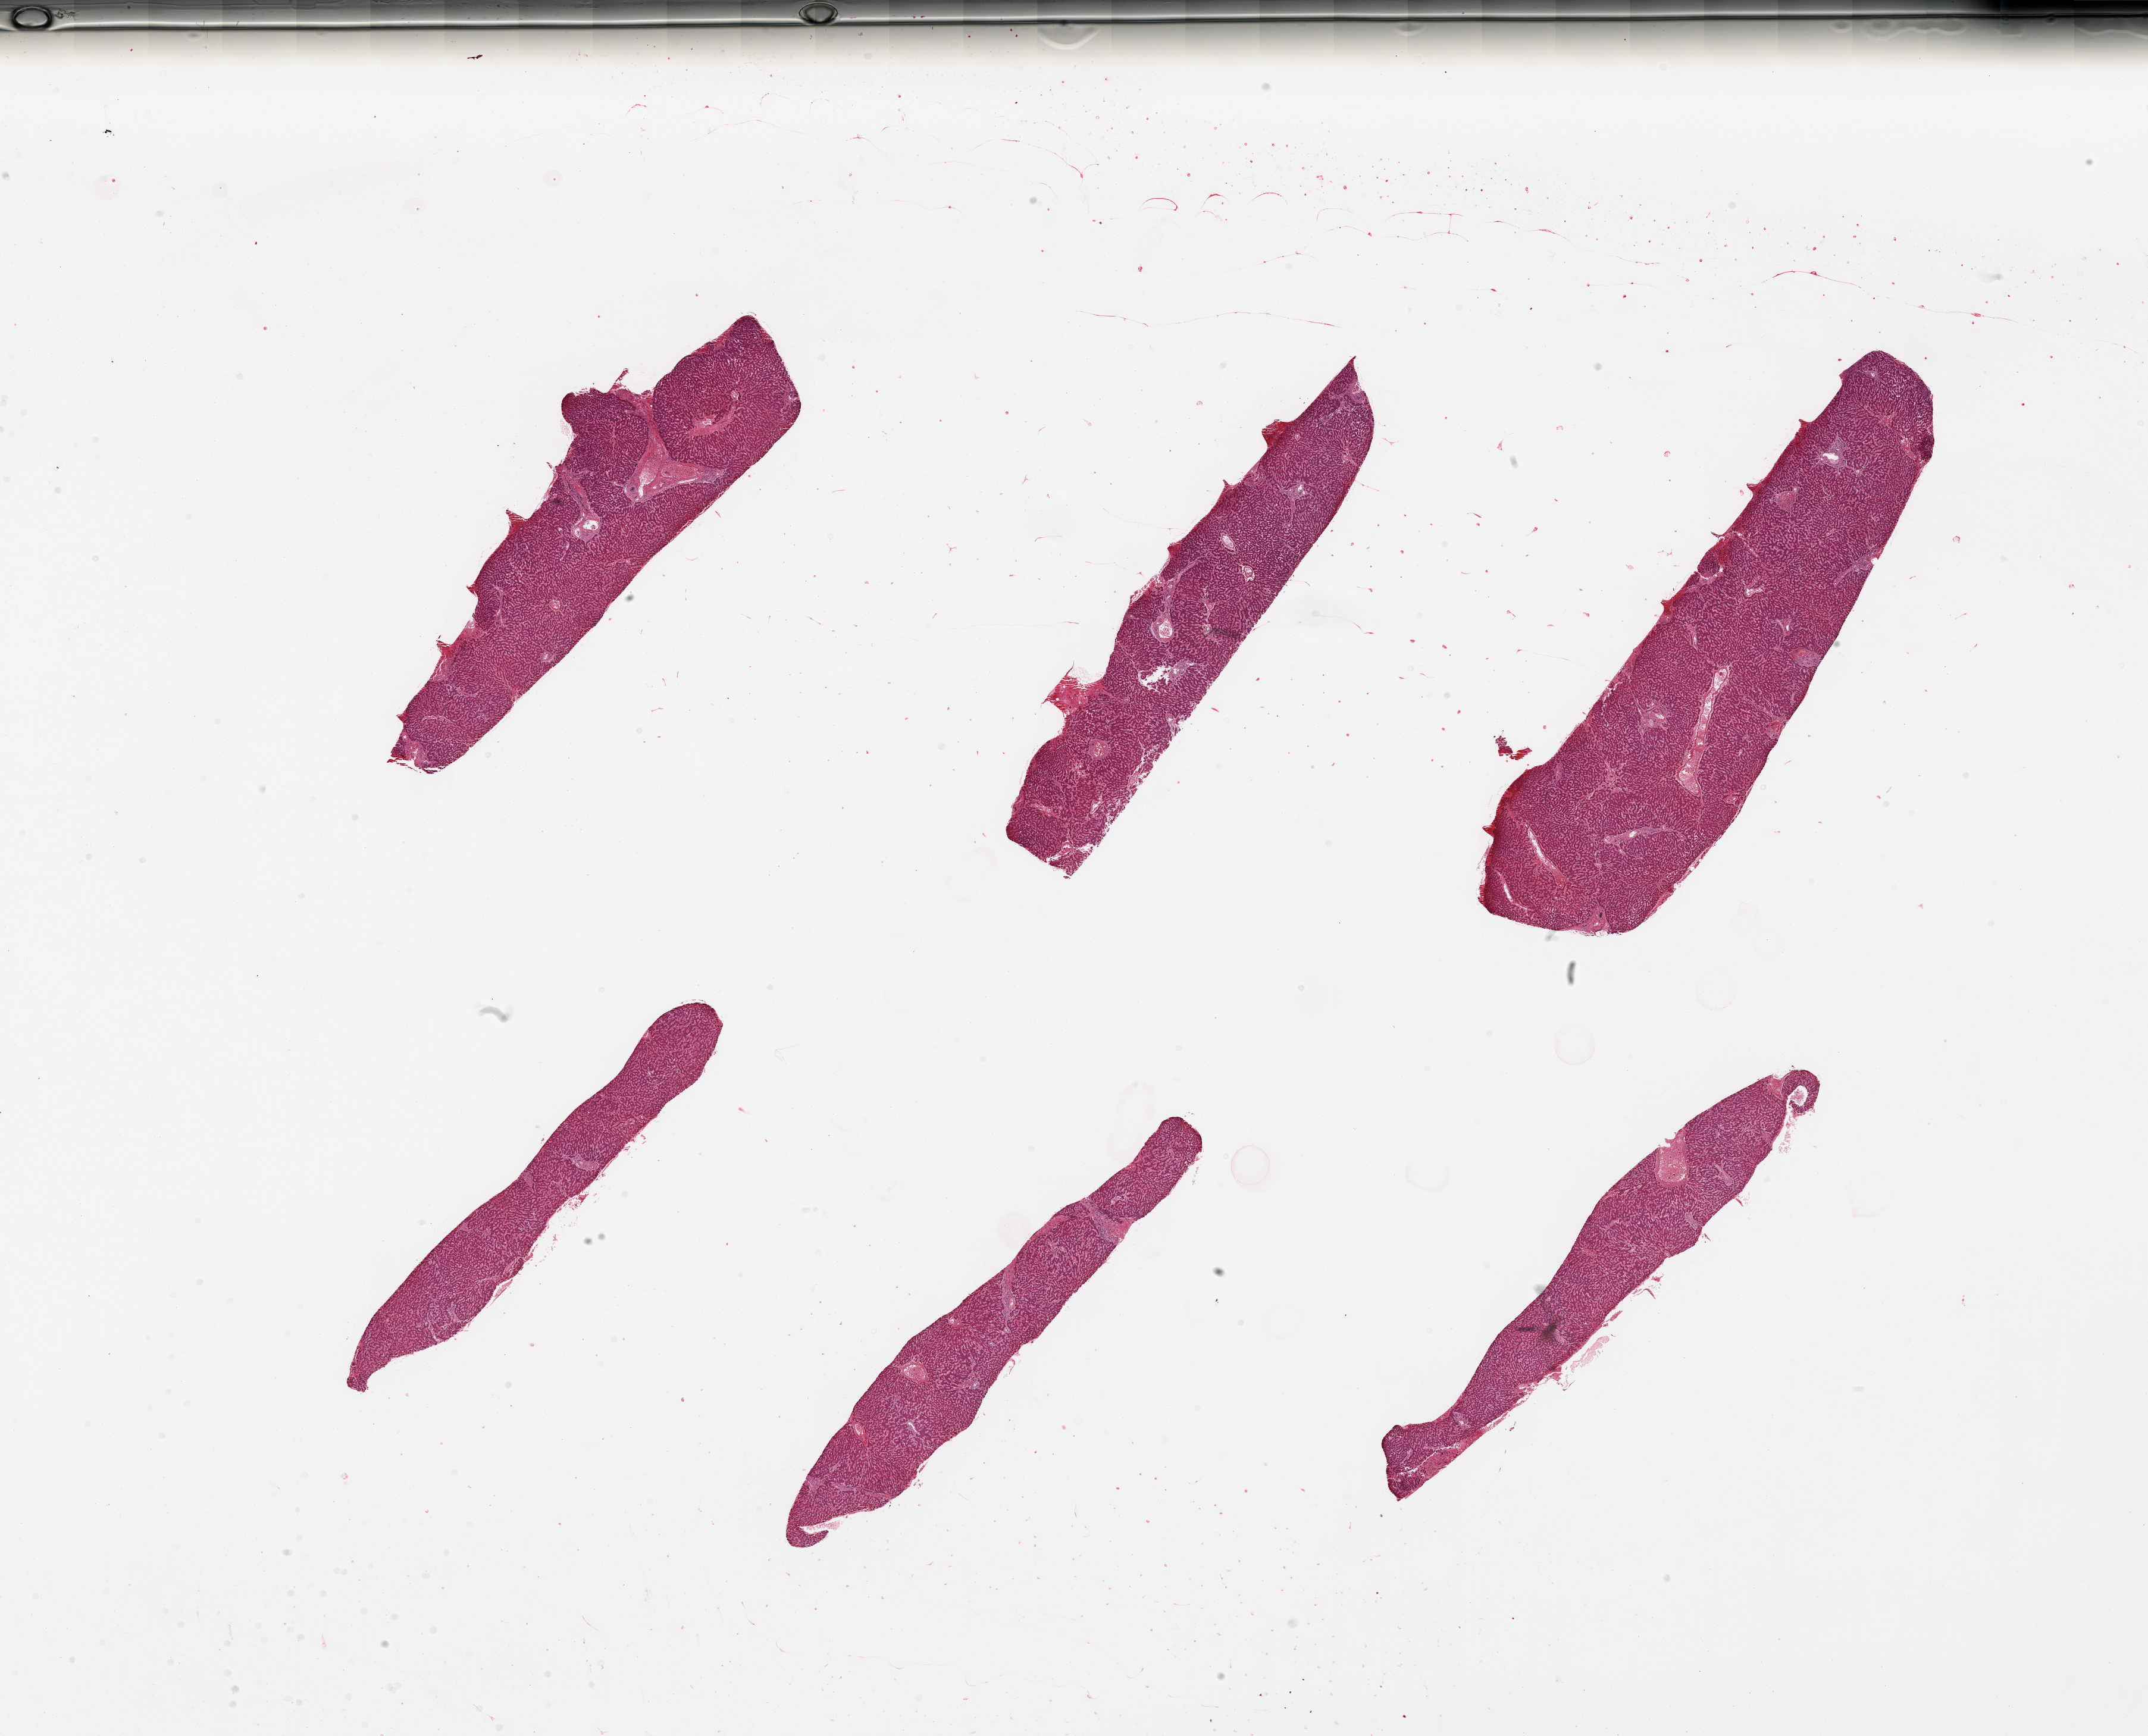
Digitized hematoxylin and eosin (H&E)-stained section — a low-resolution overview of the entire scanned area, about 28.5 x 23.1 mm (acquisition: 20x scan); PAXgene-fixed paraffin-embedded (PFPE) section; section of liver (target tissue); tissue donor sample.
• reviewer comment on this tissue sample: 6 pieces, minimal congestion, no steatosis